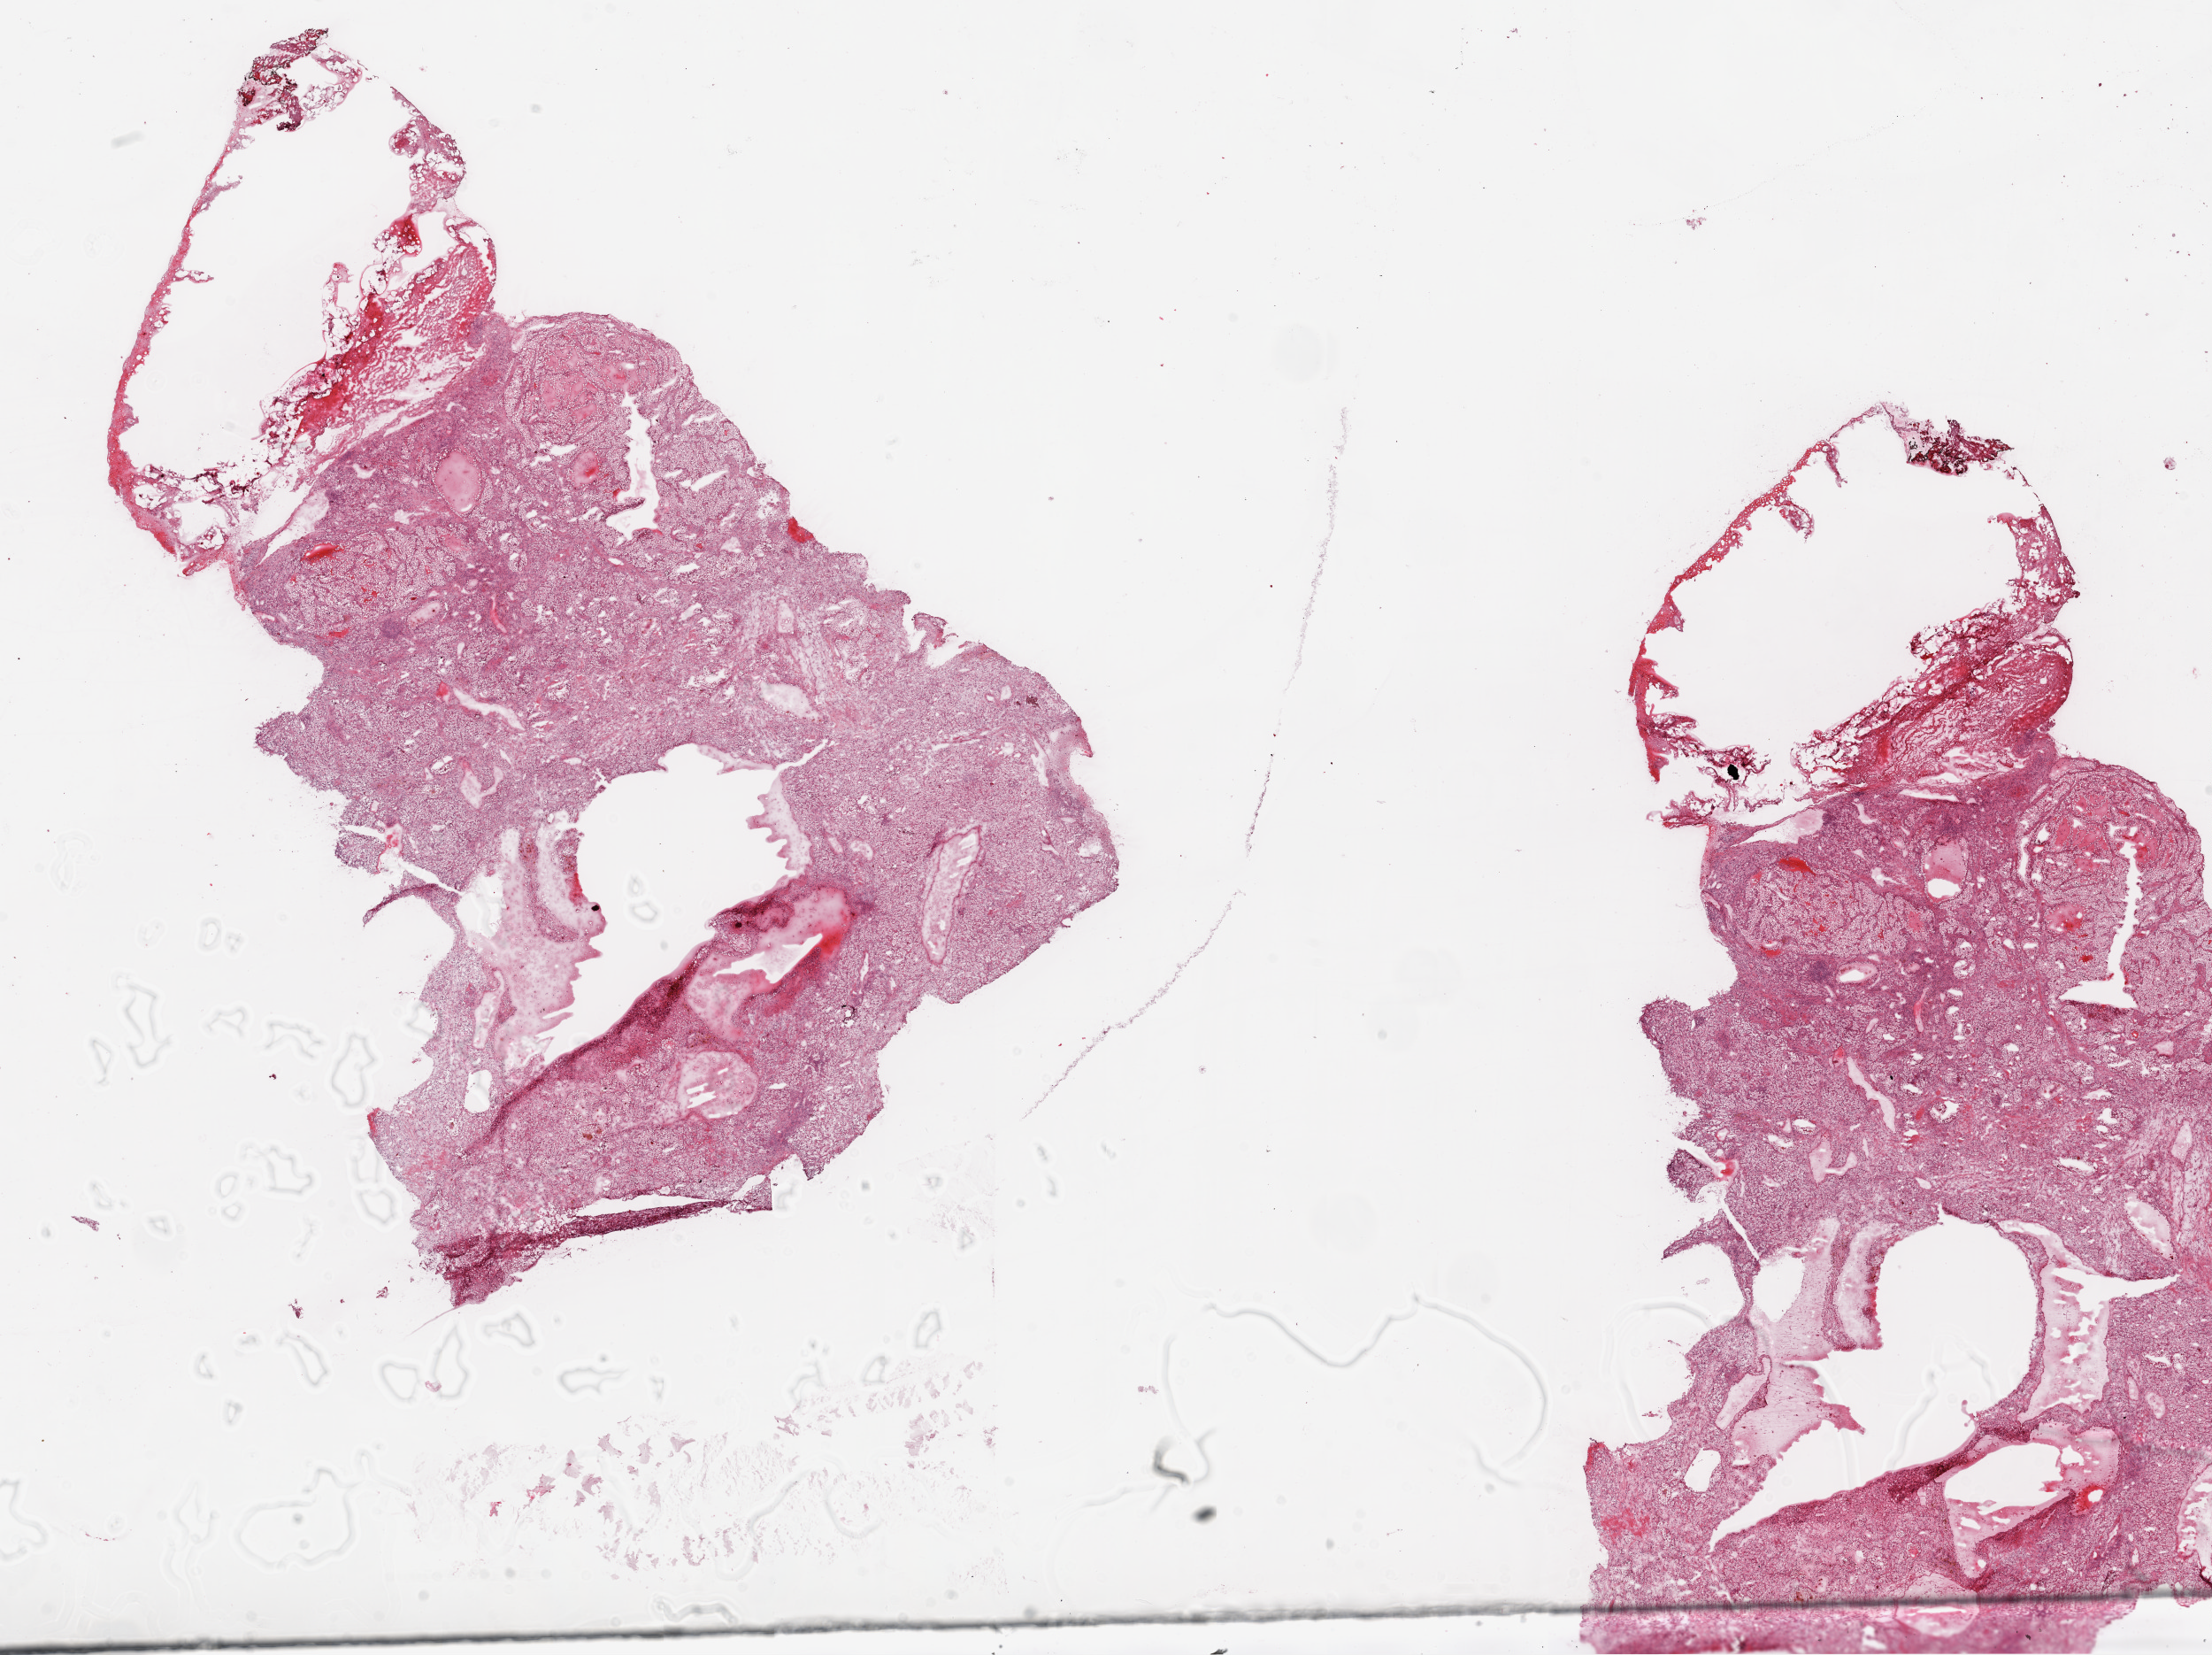
Digitized Hematoxylin and eosin (H&E) stained tissue section (whole slide), low-resolution overview of the scanned area, about 20.1 x 15.0 mm, frozen section from the top of the tissue portion, sample: primary tumour, kidney. Male patient; age at initial diagnosis 76 years. Histologic grade: G2 (moderately differentiated). Composition of this section per pathologist review: tumour cells 95%, tumour nuclei 99%, normal cells 0%, stromal cells 5%, necrosis 0%.
AJCC pathologic stage: I. TNM: T1a NX M0. Diagnosis: Clear cell adenocarcinoma, NOS. Laterality: right.